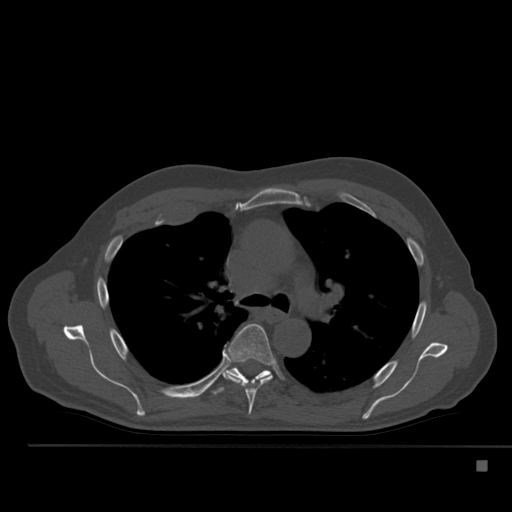
CT including the spine, one axial slice; position 359 of 517 along the scan axis; 120 kVp; bone window (W 1800 / L 400 HU); 1.5 mm slice thickness; 512 × 512 image matrix, field of view 408 × 408 mm. Patient: male, 70 years. From the clinical record (not read from this slice): primary cancer: renal.
Structures marked on this image (semi-automatic segmentation, software-assisted and operator-edited):
- T5 vertebra: bounding box [x1, y1, x2, y2] px = [220, 324, 274, 415]
- T6 vertebra: [208, 367, 270, 395]